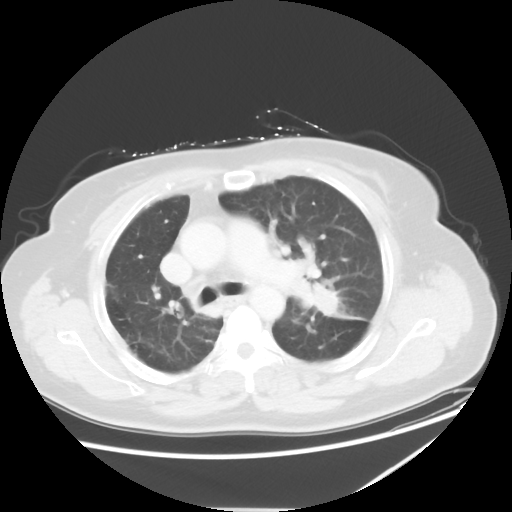
Chest CT, one axial slice. Position 37 of 54 along the scan axis. 120 kVp. Lung window (W 1500 / L -600 HU). 5 mm slice thickness. 512 × 512 image matrix, field of view 384 × 384 mm. Female patient, age 61 years. From the clinical record (not read from this slice): clinical TNM (as recorded): T1c N3 M1.
Annotated regions visible in this slice (bounding box drawn by a radiologist):
- lung tumour (recorded histology: adenocarcinoma): bounding box <305,278,372,327> (left, top, right, bottom; pixels)